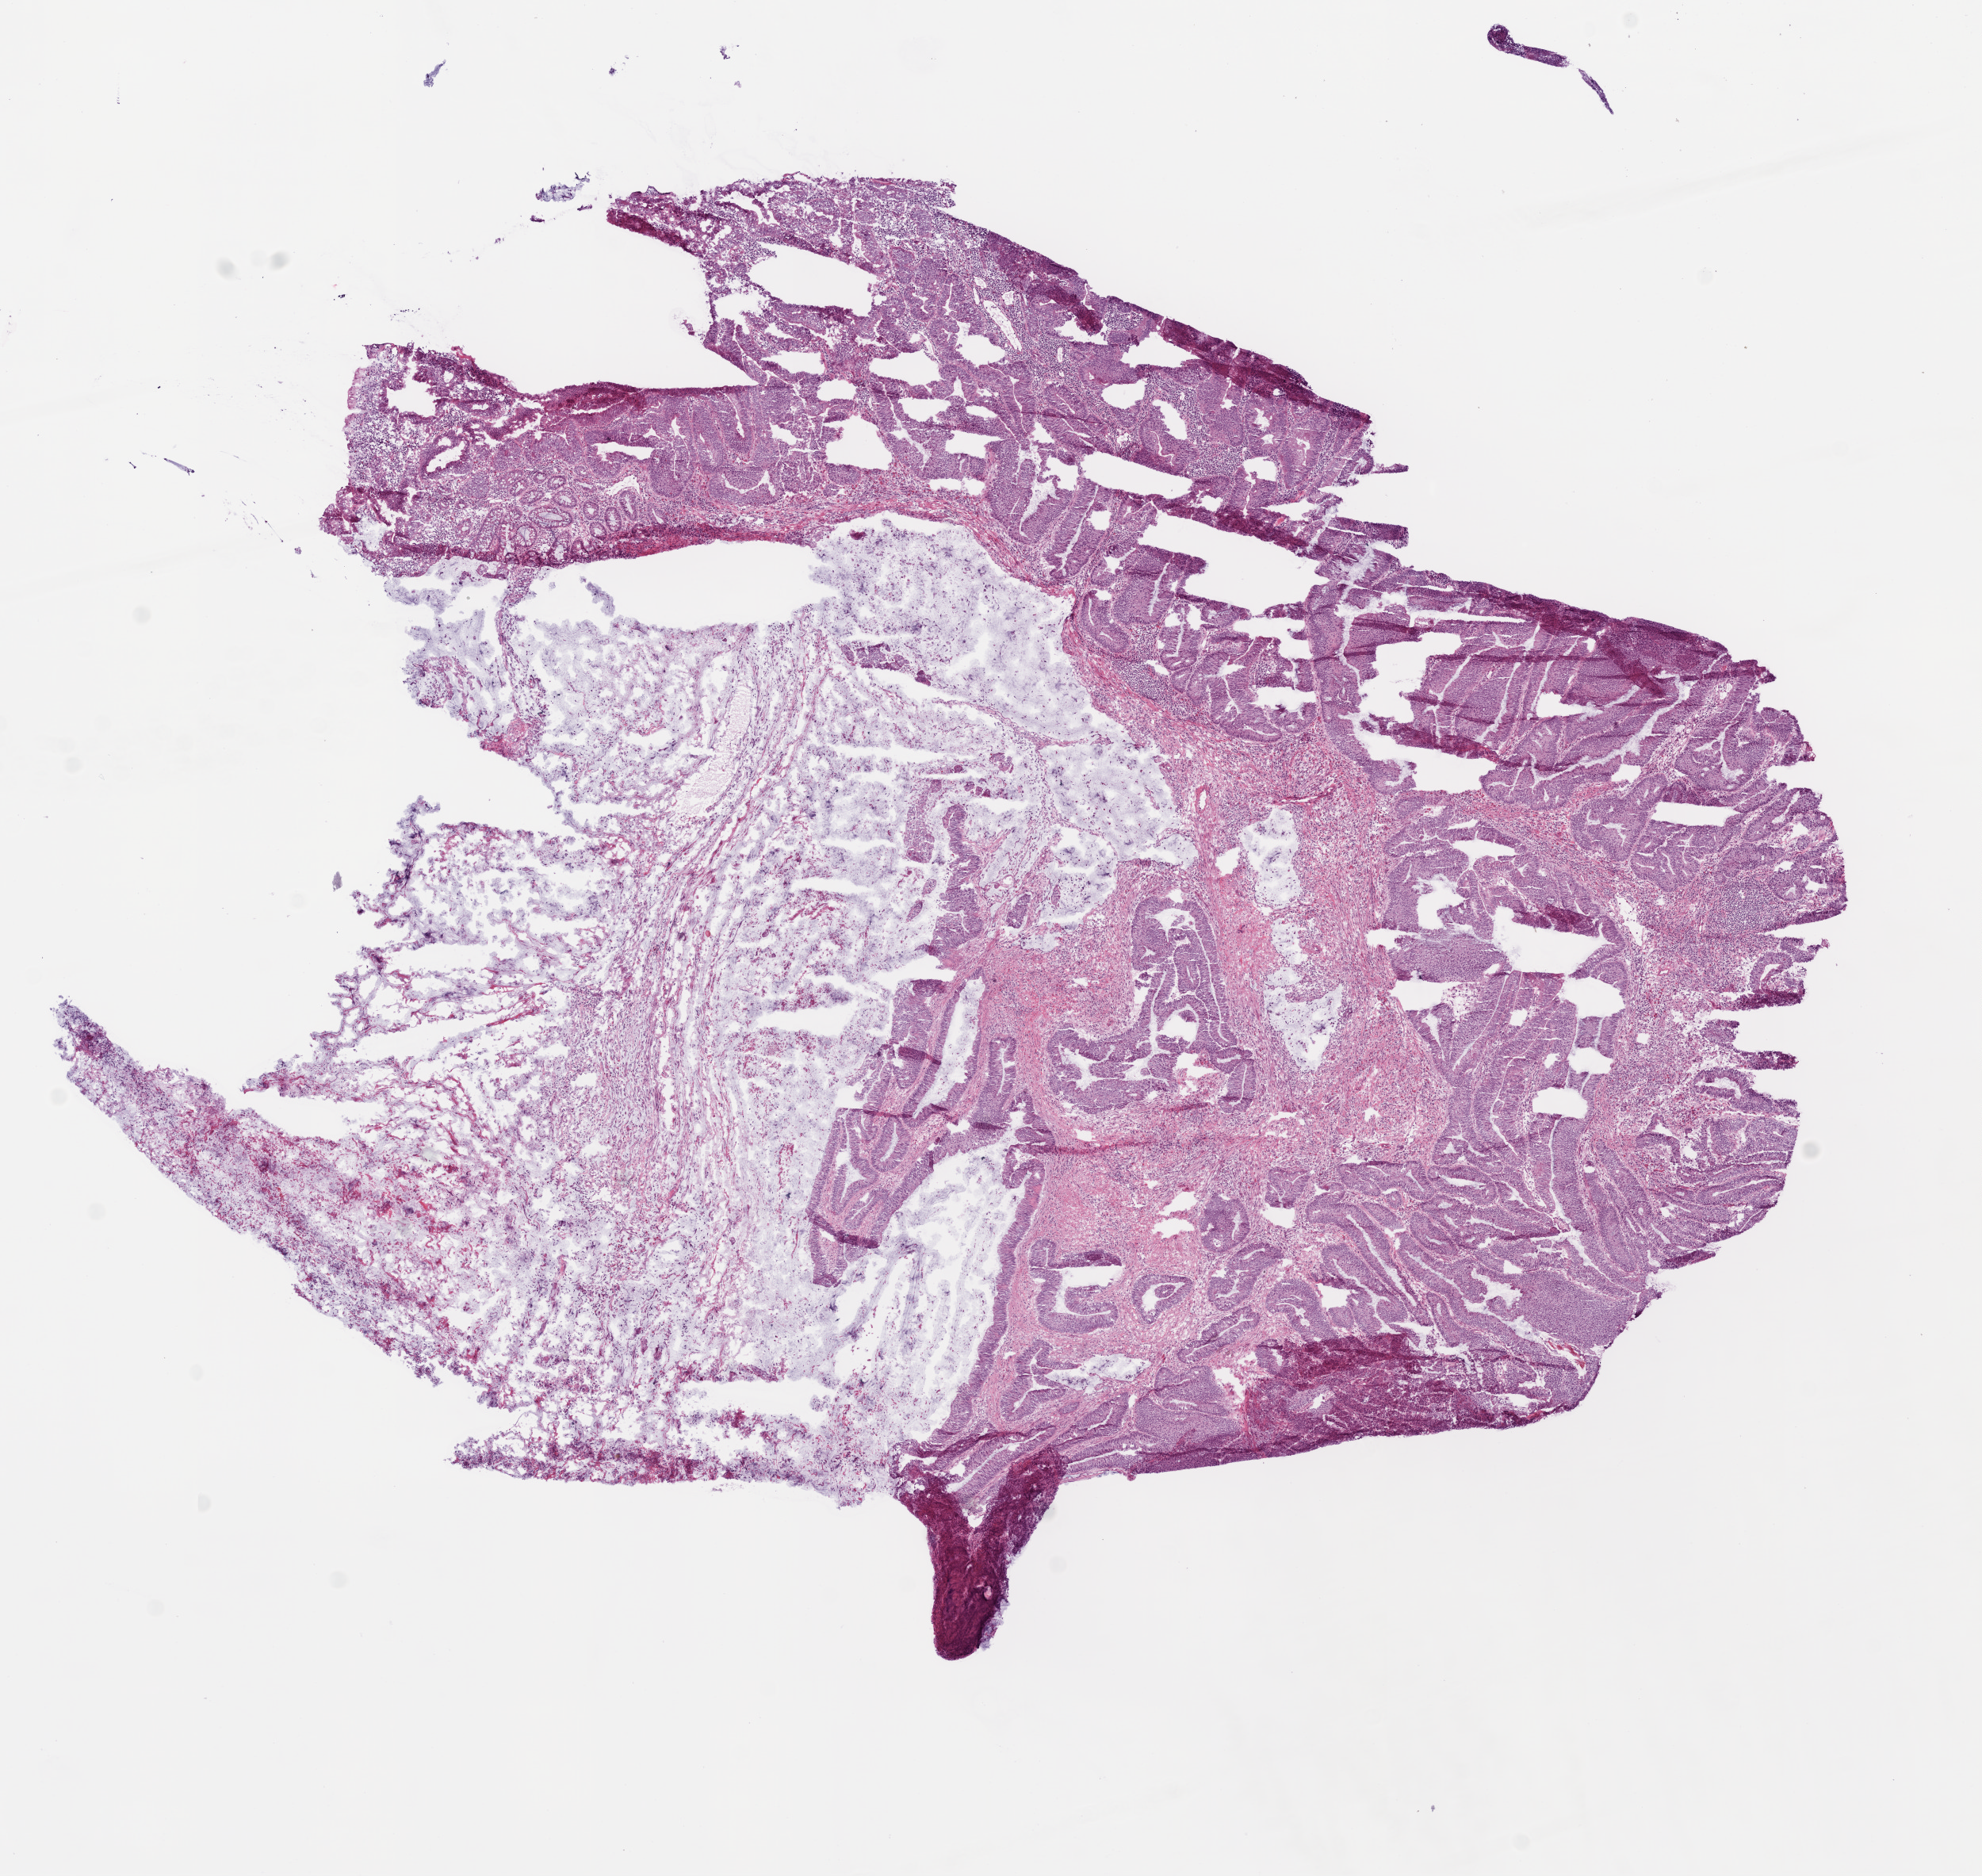
Digitized Hematoxylin and eosin (H&E) stained tissue section (whole slide) — a low-resolution overview of the entire scanned area, about 10.0 x 9.5 mm (from a 20x scan), frozen section from the bottom of the tissue portion, primary tumour sample from the colon. Male, age 88 years at initial diagnosis. Slide review estimates, as recorded: tumour cells 88%, tumour nuclei 75%, normal cells 2%, stromal cells 20%, necrosis 0%.
AJCC pathologic stage: IIA (6th edition). Lymph nodes positive (case pathology): 0 of 13 examined. TNM: T3 N0 M0. Pathologic diagnosis: Mucinous adenocarcinoma.